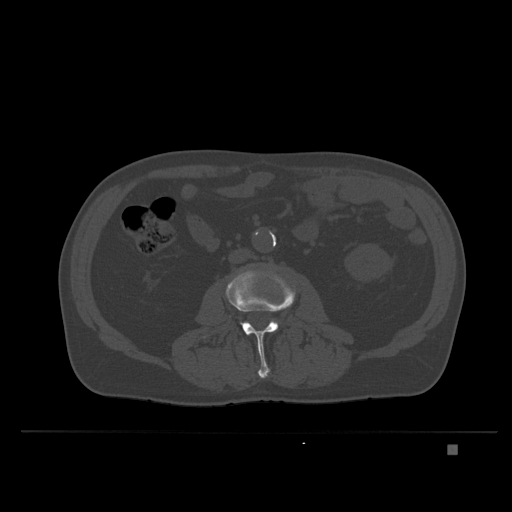
CT including the spine, one axial slice; slice 94 of 435 in the series (ordered by position); bone window (W 1800 / L 400 HU); 512 × 512 image matrix. Male patient, age 73 years. Case-level facts recorded for this patient, not image findings: primary cancer: skin.
Annotated regions visible in this slice (semi-automatic segmentation, software-assisted and operator-edited):
- L2 vertebra: bounding box (x1, y1, x2, y2) in pixels: (258, 374, 266, 378)
- L3 vertebra: (203, 269, 296, 378)